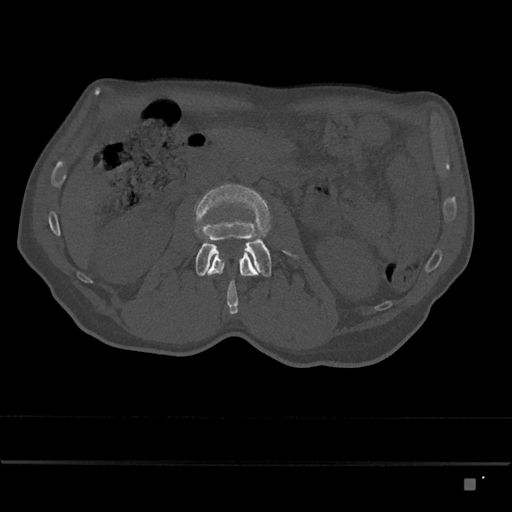
CT including the spine, one axial slice. Slice 436 of 797 in the series (ordered by position). Reconstruction kernel Br40s/3. 120 kVp. Bone window (W 1800 / L 400 HU). 0.5 mm slice thickness. 512 × 512 image matrix, field of view 390 × 390 mm. Patient: male, 72 years. Case-level facts recorded for this patient, not image findings: primary cancer: prostate.
Structures marked on this image (semi-automatic segmentation, software-assisted and operator-edited):
- L2 vertebra: bounding box <205,249,258,314> (left, top, right, bottom; pixels)
- L3 vertebra: <194,184,298,277>